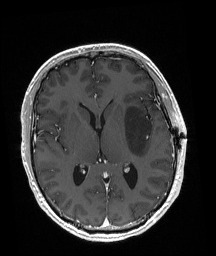
Brain MRI from a brain-tumour surgery series, one axial slice; slice 97 of 192 in the series (ordered by position); T1-weighted post-contrast; 1 mm slice thickness; 216 × 256 image matrix, field of view 211 × 250 mm. From the clinical record (not read from this slice): histopathology: Astrocytoma; WHO grade: 3; IDH mutation: yes; tumour location: Left Posterior Frontal.
Structures marked on this image (manually delineated by an expert):
- tumour: box from (x=124, y=107) to (x=152, y=157) px